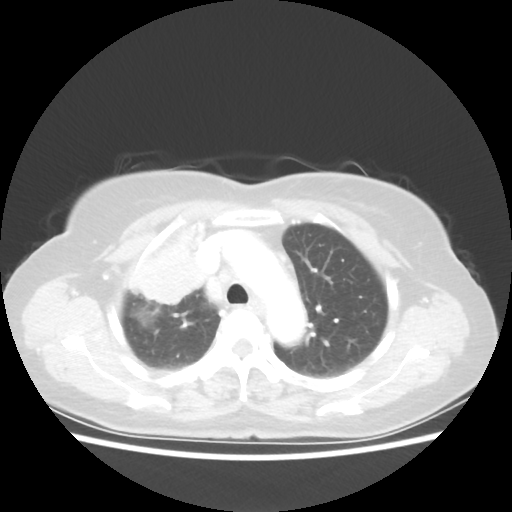
Chest CT, one axial slice; position 40 of 55 along the scan axis; reconstruction kernel STANDARD; lung window (W 1500 / L -600 HU); 5 mm slice thickness; 512 × 512 image matrix, field of view 337 × 337 mm. Patient: female, 62 years. Case-level facts recorded for this patient, not image findings: clinical TNM (as recorded): T4 N3 M0.
Annotated regions visible in this slice (rectangle marked by the reading radiologist):
- lung tumour (recorded histology: squamous cell carcinoma): bounding box <131,240,206,312> (left, top, right, bottom; pixels)